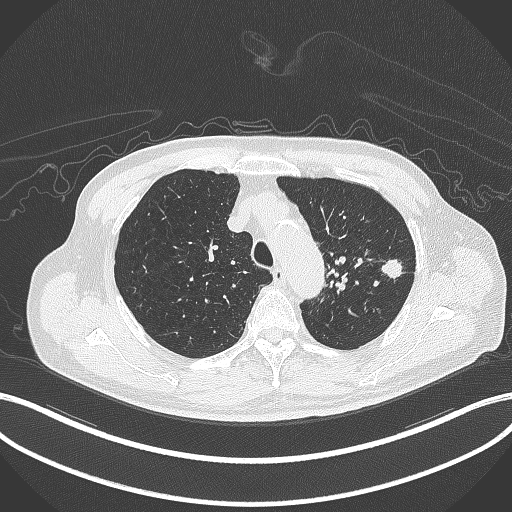
Chest CT, one axial slice. Slice 341 of 417 in the series (ordered by position). Reconstruction kernel B70f. 120 kVp. Lung window (W 1500 / L -600 HU). 1 mm slice thickness. 512 × 512 image matrix, field of view 400 × 400 mm. Male patient, age 77 years. From the clinical record (not read from this slice): clinical TNM (as recorded): T3 N1 M0.
Annotated regions visible in this slice (bounding box drawn by a radiologist):
- lung tumour (recorded histology: adenocarcinoma): bounding box (x1, y1, x2, y2) in pixels: (379, 254, 405, 283)